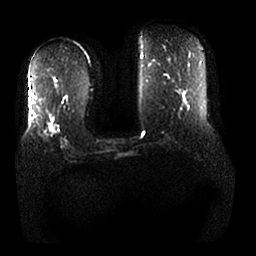
Breast MRI, one axial slice; position 10 of 25 along the scan axis; diffusion-weighted series; image 2 of 4 stored at this slice position (different b-values; order by instance number); 1.5 T; 4 mm slice thickness; 256 × 256 image matrix, field of view 380 × 380 mm. Female patient.
Annotated regions visible in this slice (outlined manually by an expert reader):
- tumour on diffusion-weighted imaging: bounding box [x1, y1, x2, y2] px = [48, 123, 55, 134]